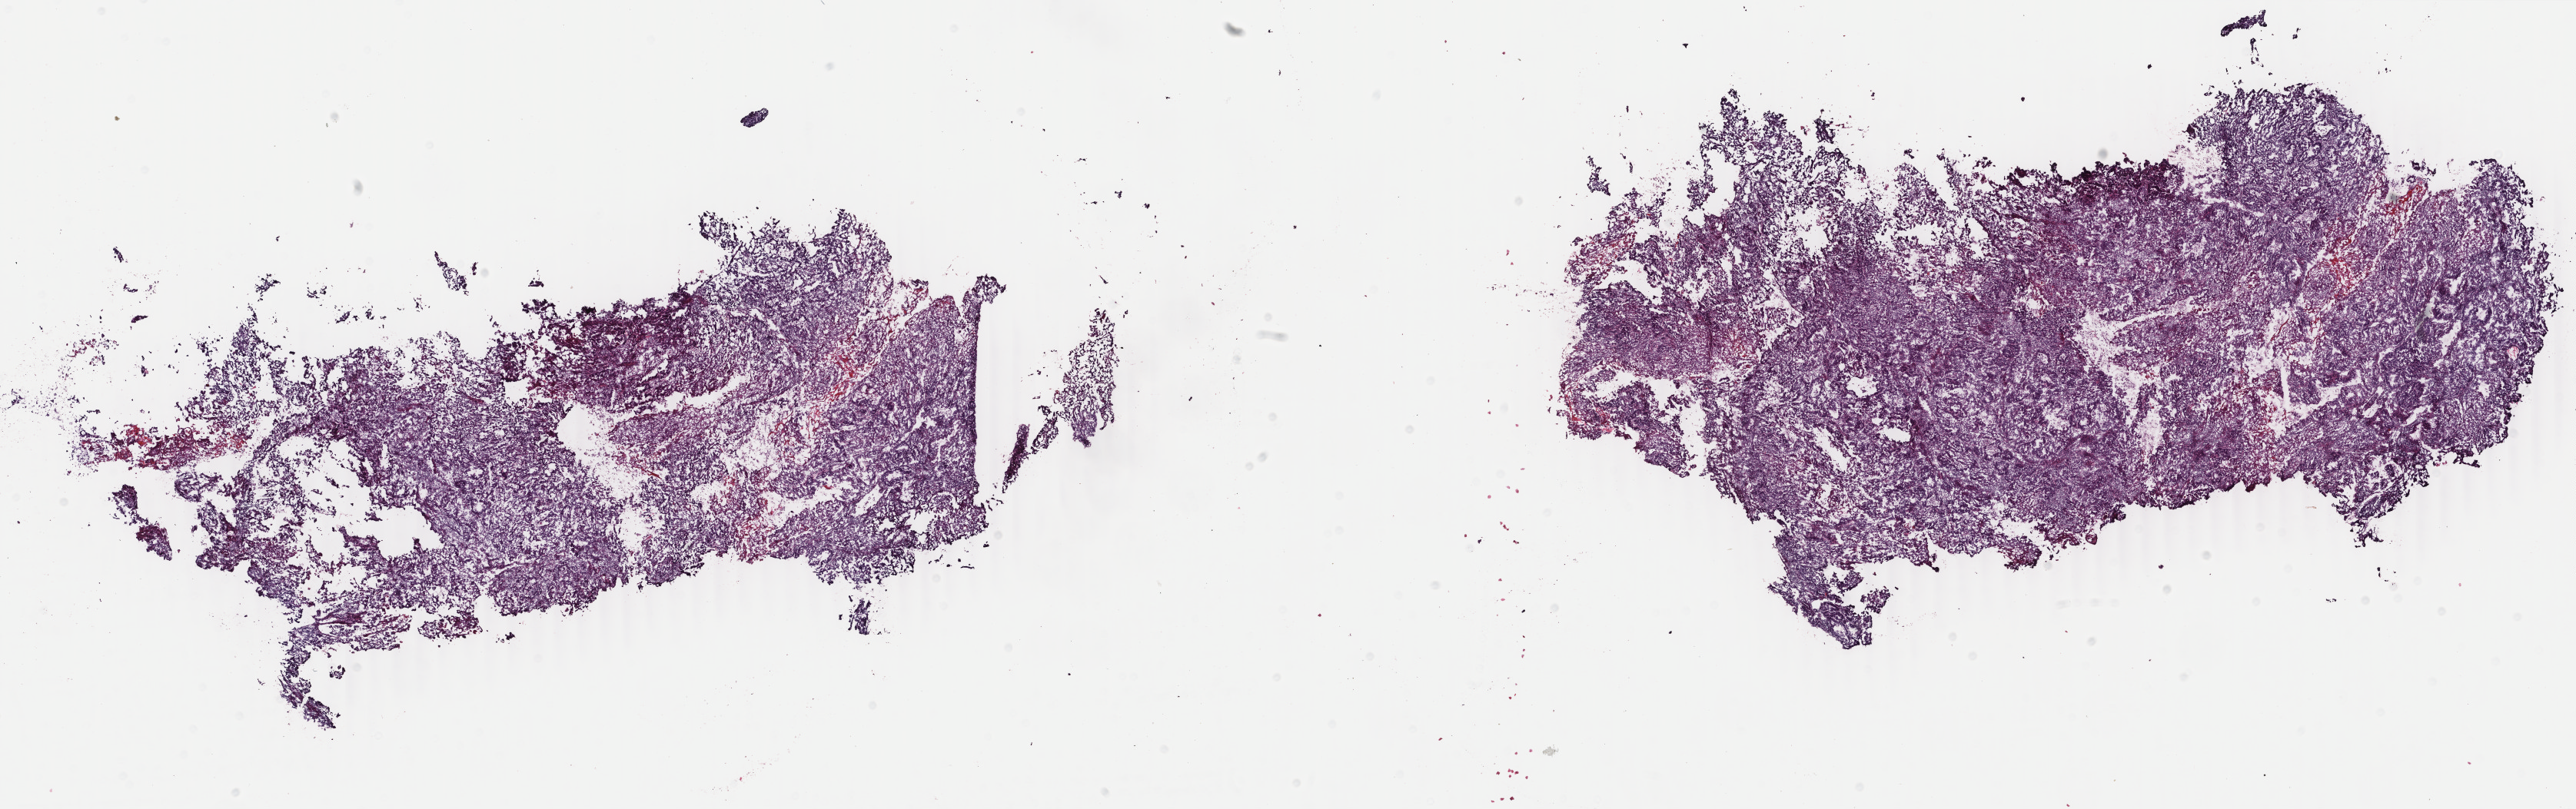
Digitized Hematoxylin and eosin (H&E) stained tissue section (whole slide) — shown as a low-resolution overview of the whole scanned area (about 26.7 x 8.4 mm); frozen section; uterus, primary tumour sample. Female patient; age at initial diagnosis 58 years. Histologic grade: G1 (well differentiated). Pathologist review of this section (percent, as recorded): tumour cells 70%, tumour nuclei 70%, normal cells 0%, stromal cells 20%, necrosis 10%. Inflammatory infiltration, as recorded: lymphocyte infiltration 40%, monocyte infiltration 25%, neutrophil infiltration 30%.
- FIGO stage: IB
- pathologic diagnosis: Endometrioid adenocarcinoma, NOS (endometrium)